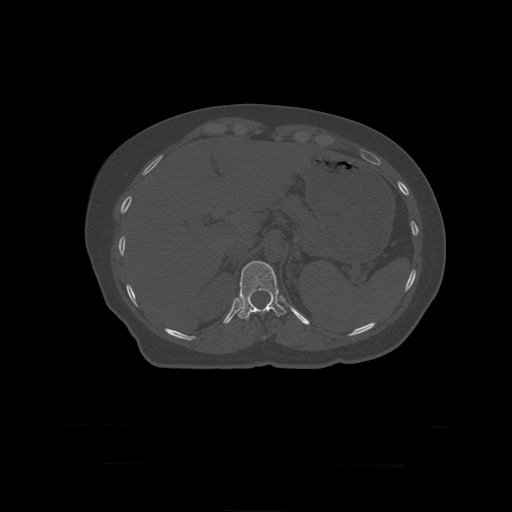
CT including the spine, one axial slice. Slice 202 of 399 in the series (ordered by position). Reconstruction kernel STANDARD. Bone window (W 1800 / L 400 HU). 512 × 512 image matrix, field of view 450 × 450 mm. Patient age 41 years. Case-level facts recorded for this patient, not image findings: primary cancer: breast.
Annotated regions visible in this slice (semi-automatically segmented with operator editing):
- T11 vertebra: box from (x=264, y=336) to (x=266, y=339) px
- T12 vertebra: (x=238, y=261)–(x=287, y=321)